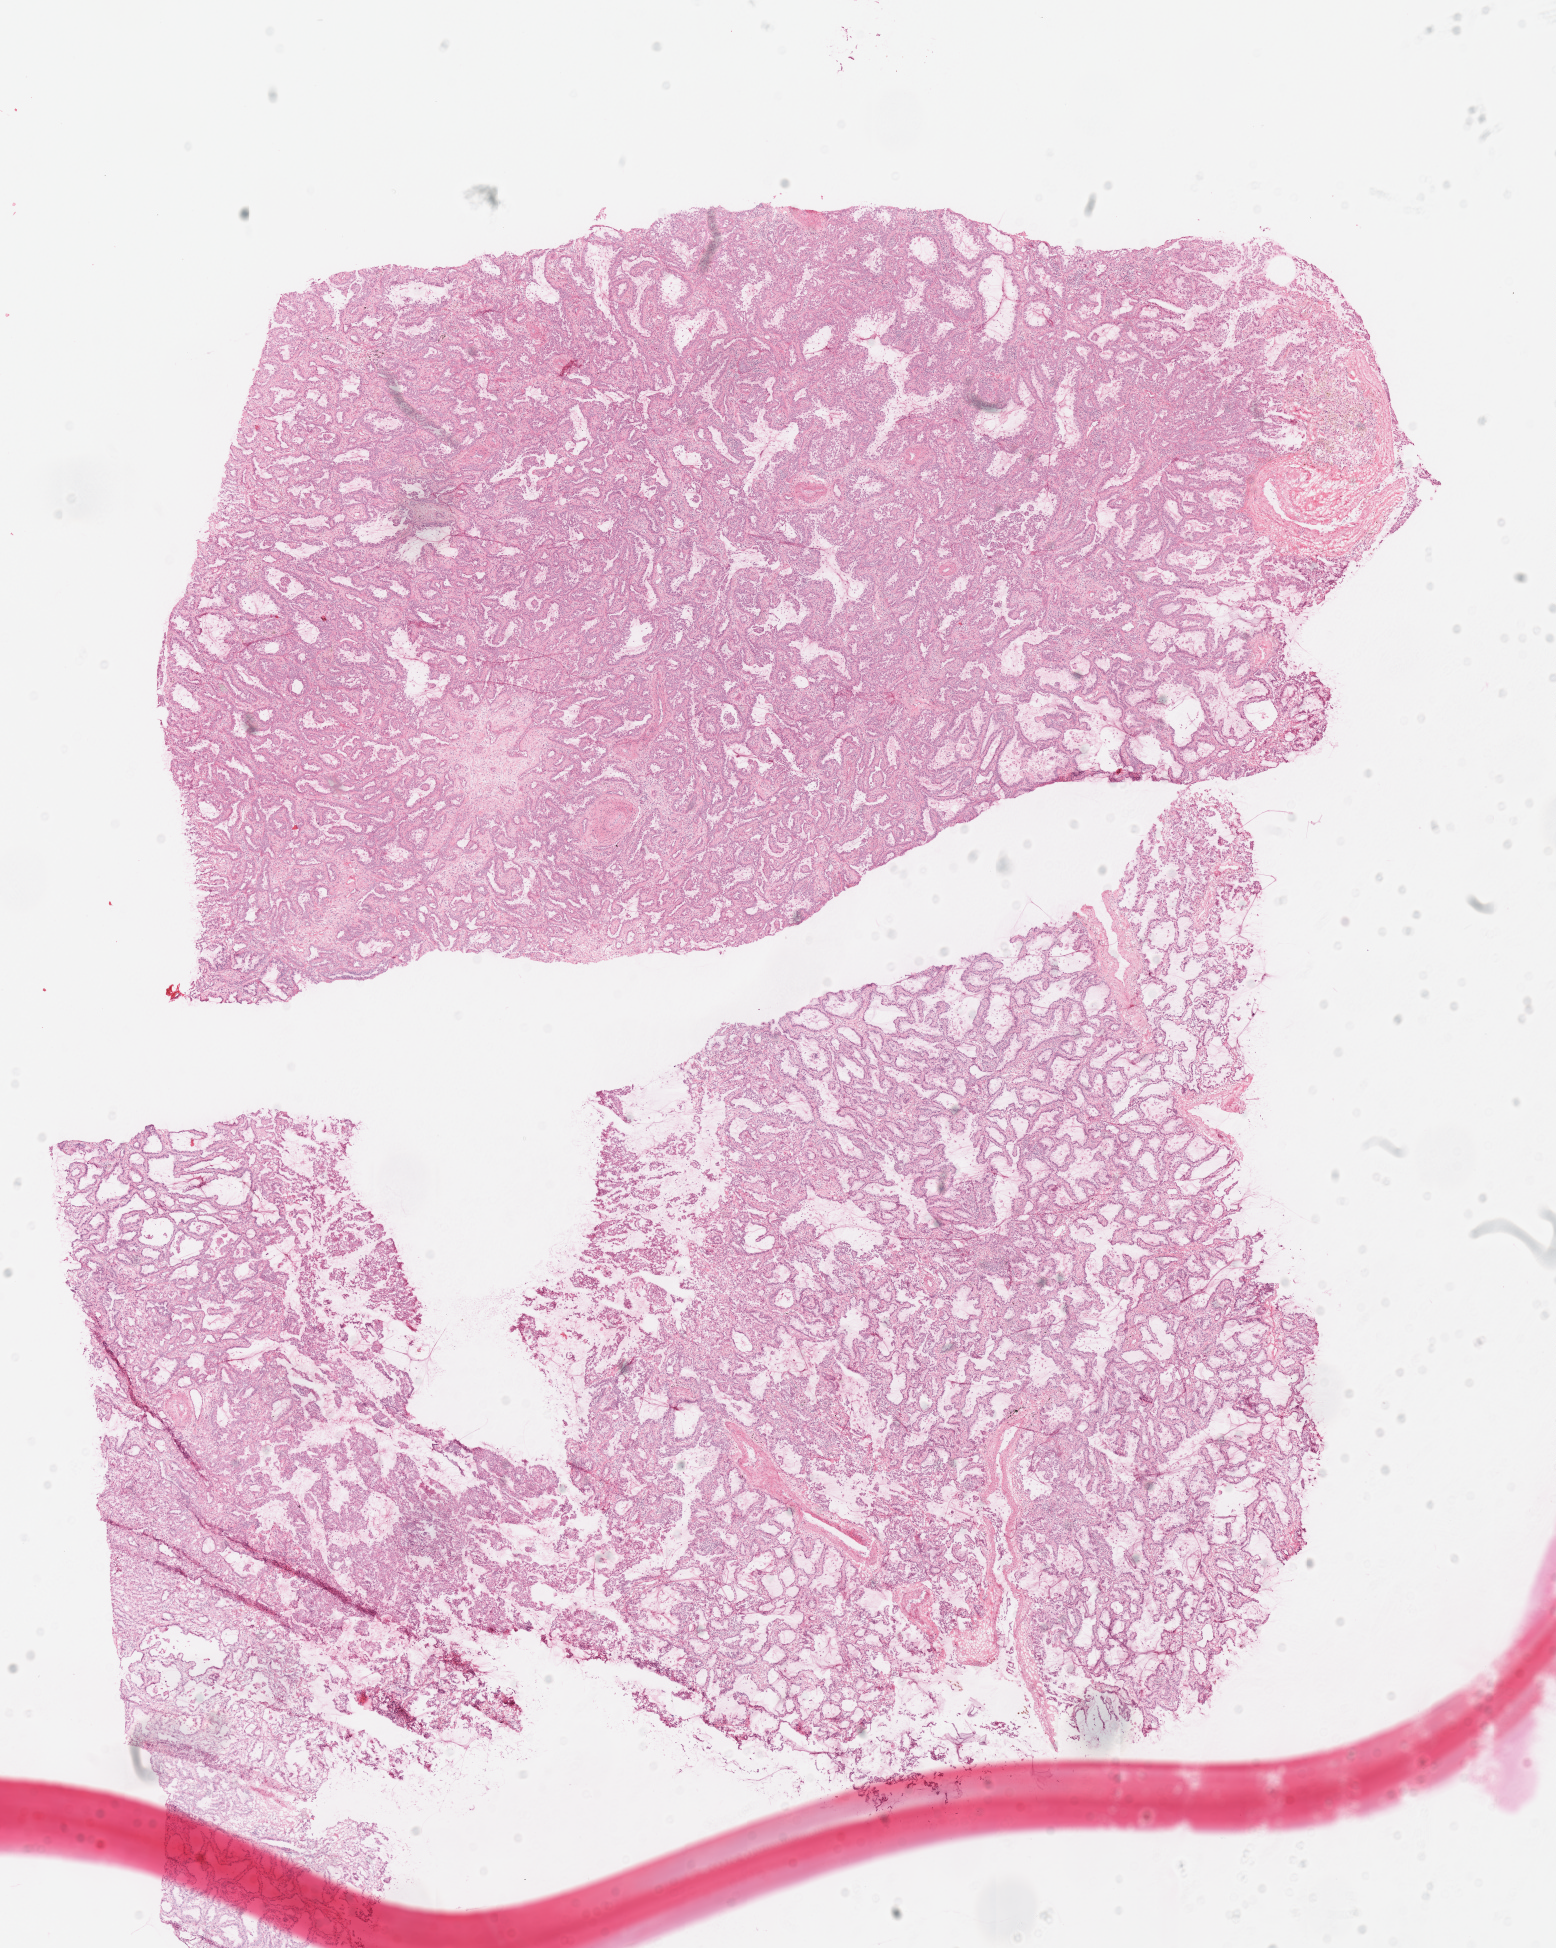
H&E-stained whole-slide image, whole scanned area (about 12.2 x 15.3 mm, from a 40x scan) shown as a low-resolution overview; frozen section; sample: primary tumour, lung. Female patient; age at initial diagnosis 61 years. Slide review estimates, as recorded: tumour cells 100%, tumour nuclei 80%, normal cells 0%, stromal cells 0%, necrosis 0%. Inflammatory infiltration, as recorded: lymphocyte infiltration 10%, monocyte infiltration 0%, neutrophil infiltration 0%.
• laterality: right
• AJCC pathologic stage: IIIA (7th edition)
• histologic diagnosis: Adenocarcinoma with mixed subtypes